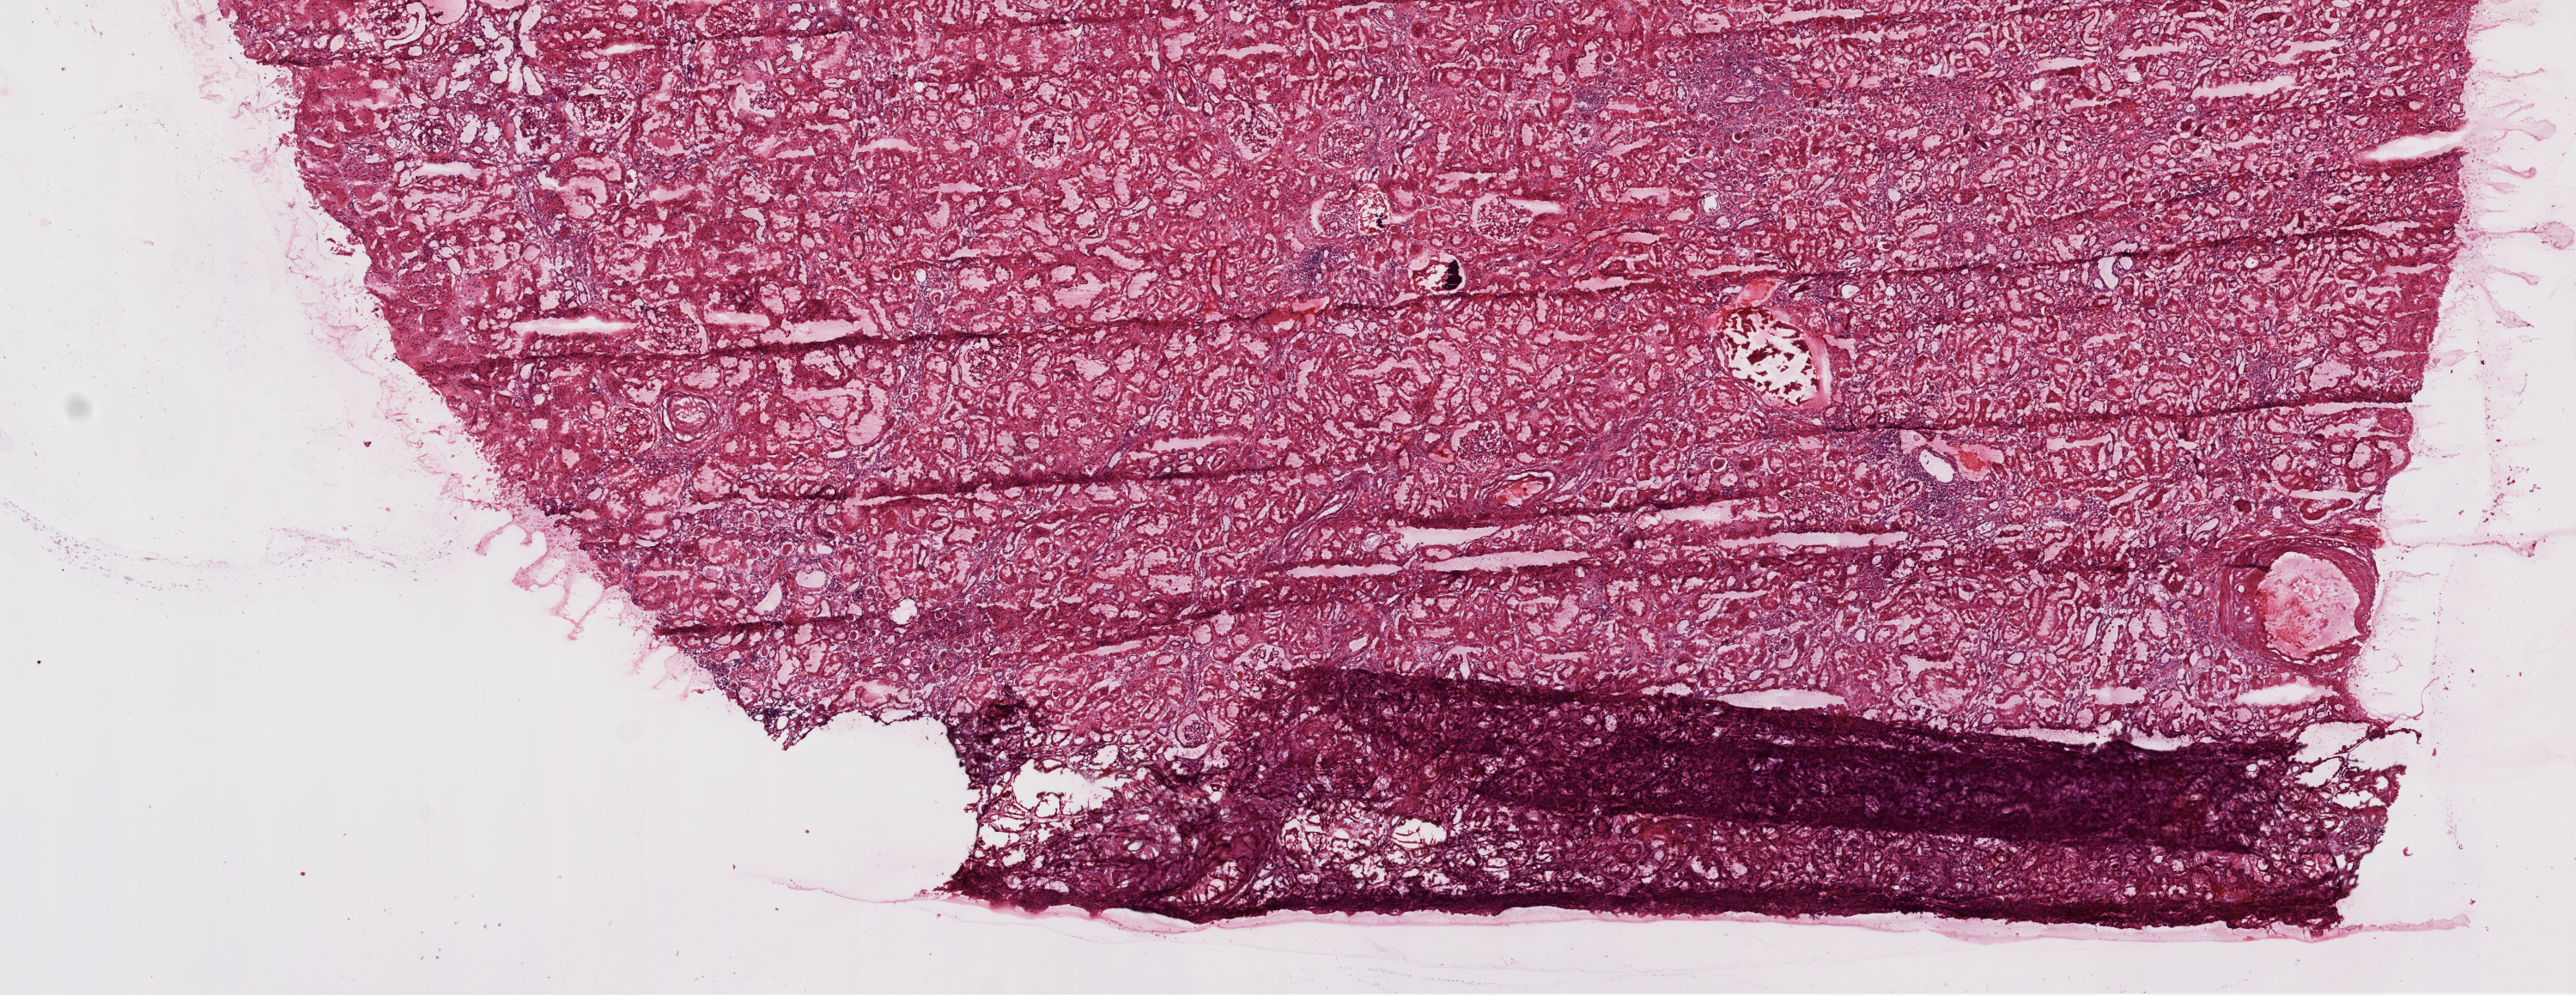
Digitized Hematoxylin and eosin (H&E) stained tissue section (whole slide), low-resolution overview of the scanned area, about 12.0 x 4.7 mm; frozen section from the top of the tissue portion; sample: solid tissue normal (non-tumour tissue), kidney. Female patient; age at initial diagnosis 80 years.
This section: solid tissue normal (non-tumour) sample from the same patient. Patient diagnosis: Clear cell adenocarcinoma, NOS.